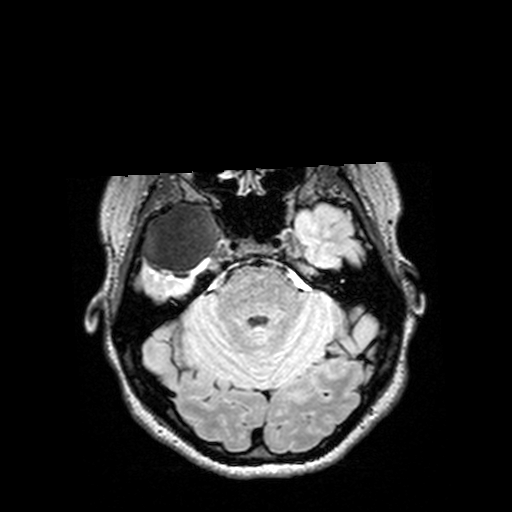
Brain MRI from a brain-tumour surgery series, one axial slice. Slice 103 of 144 in the series (ordered by position). T2 FLAIR. 1 mm slice thickness. 512 × 512 image matrix. From the clinical record (not read from this slice): histopathology: Astrocytoma; WHO grade: 3; IDH mutation: yes.
Structures marked on this image (expert manual segmentation):
- tumour: bounding box (x1, y1, x2, y2) in pixels: (126, 201, 232, 278)